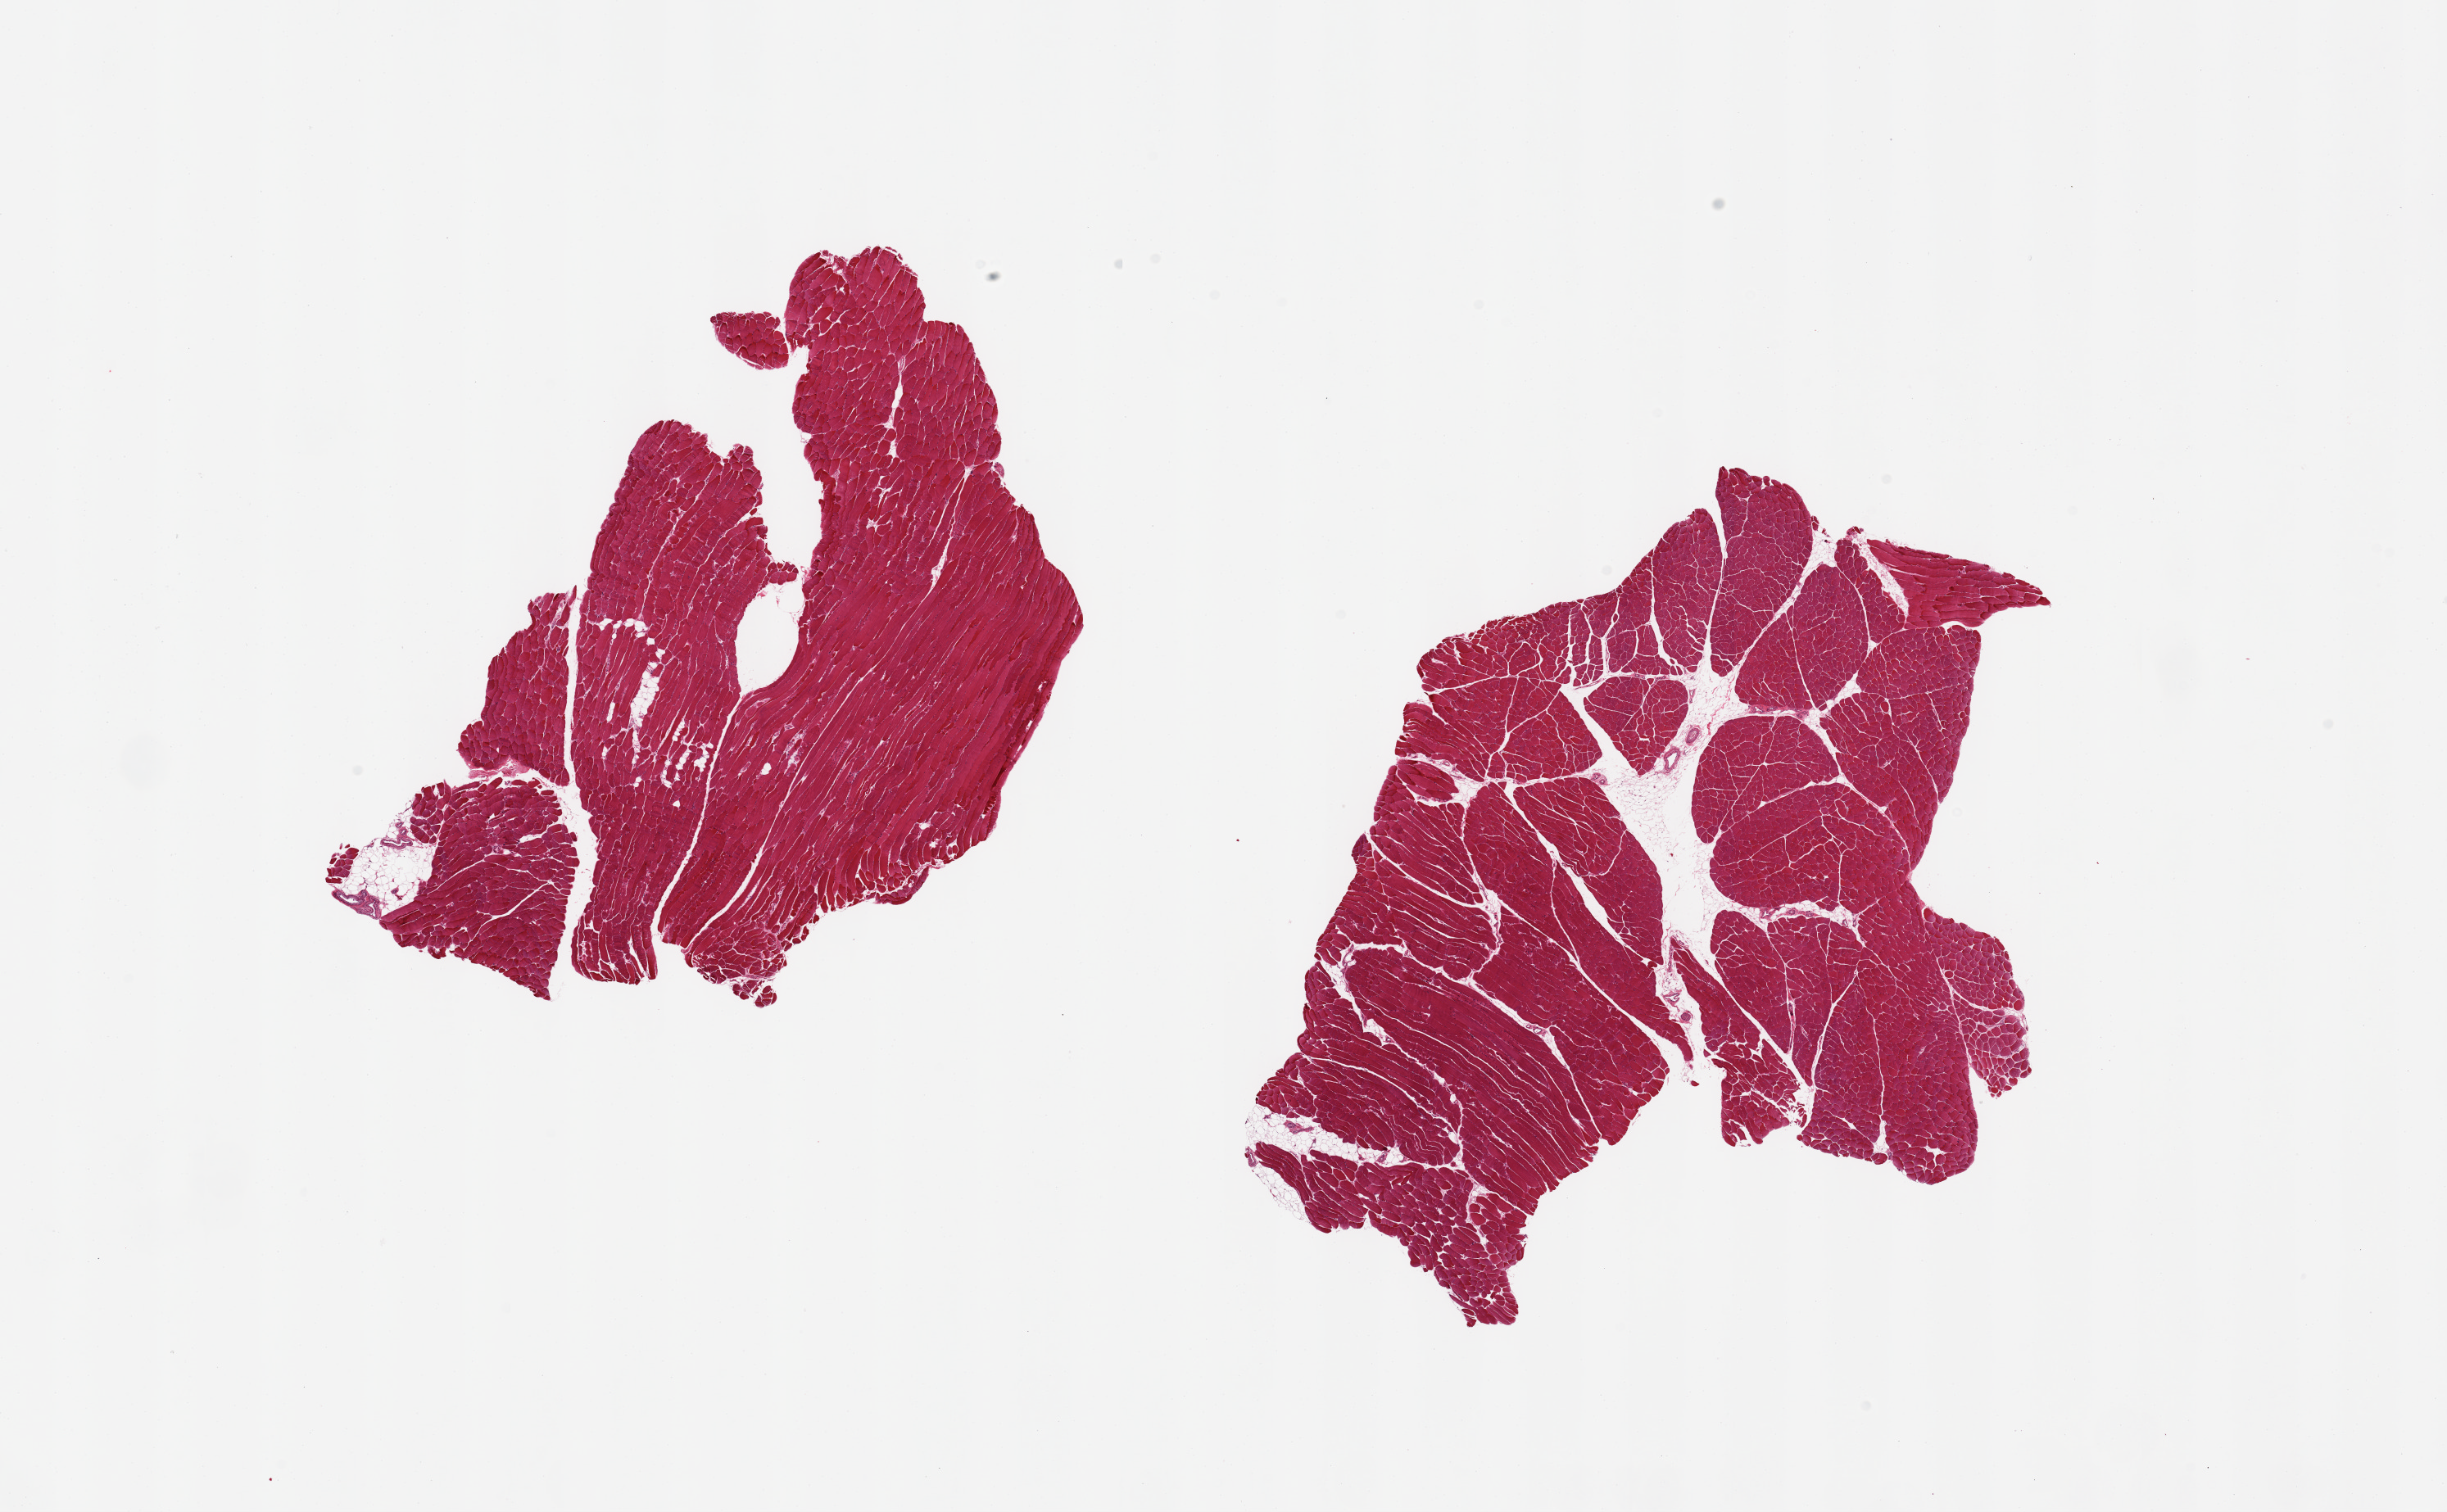
Digitized hematoxylin and eosin (H&E)-stained section, brightfield, whole scanned area (about 23.6 x 14.6 mm) shown as a low-resolution overview; PAXgene-fixed, paraffin-embedded tissue; section of skeletal muscle (target tissue); tissue donor sample. Male donor.
Review note (as recorded): 2 pieces, less than ~5% interstitial fat/vascular elements.